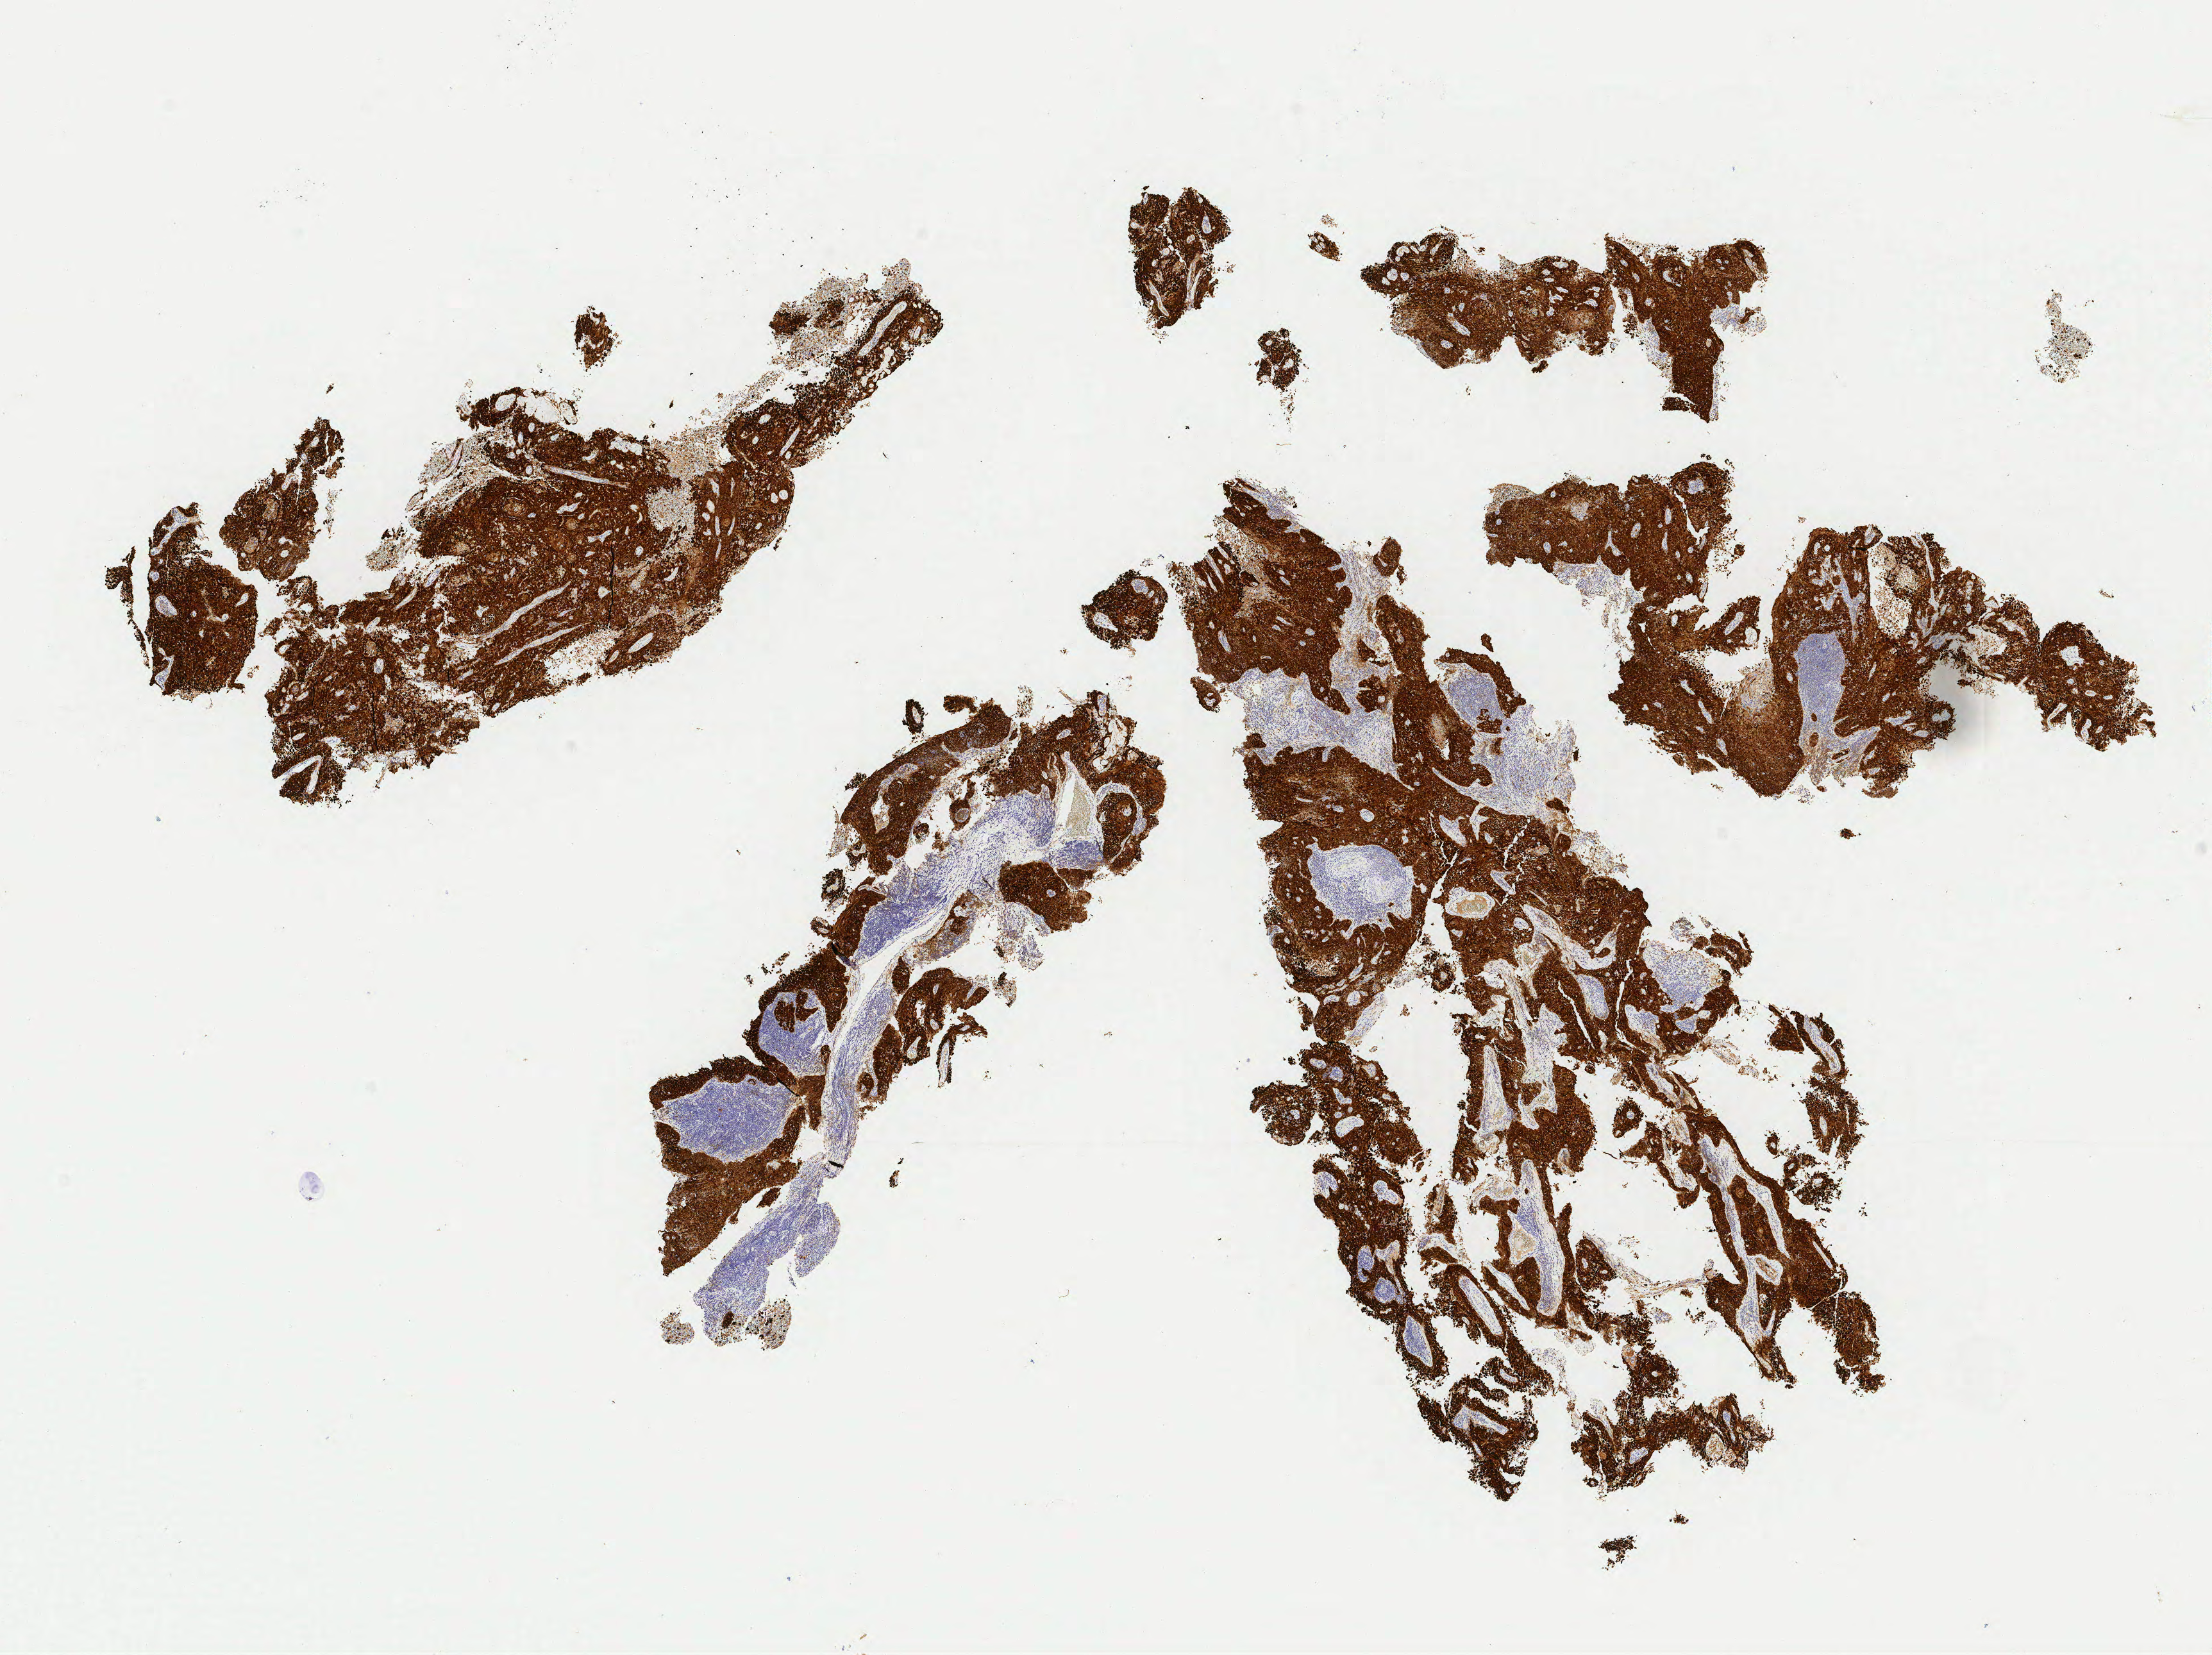
IHC for p16 (p16INK4a), whole-slide image — a low-resolution overview of the entire scanned area, about 13.7 x 10.2 mm. Tumor tissue. Anatomic site: cervix. Patient: female, aged 58.
Histologic diagnosis: Squamous cell carcinoma, keratinizing, NOS.